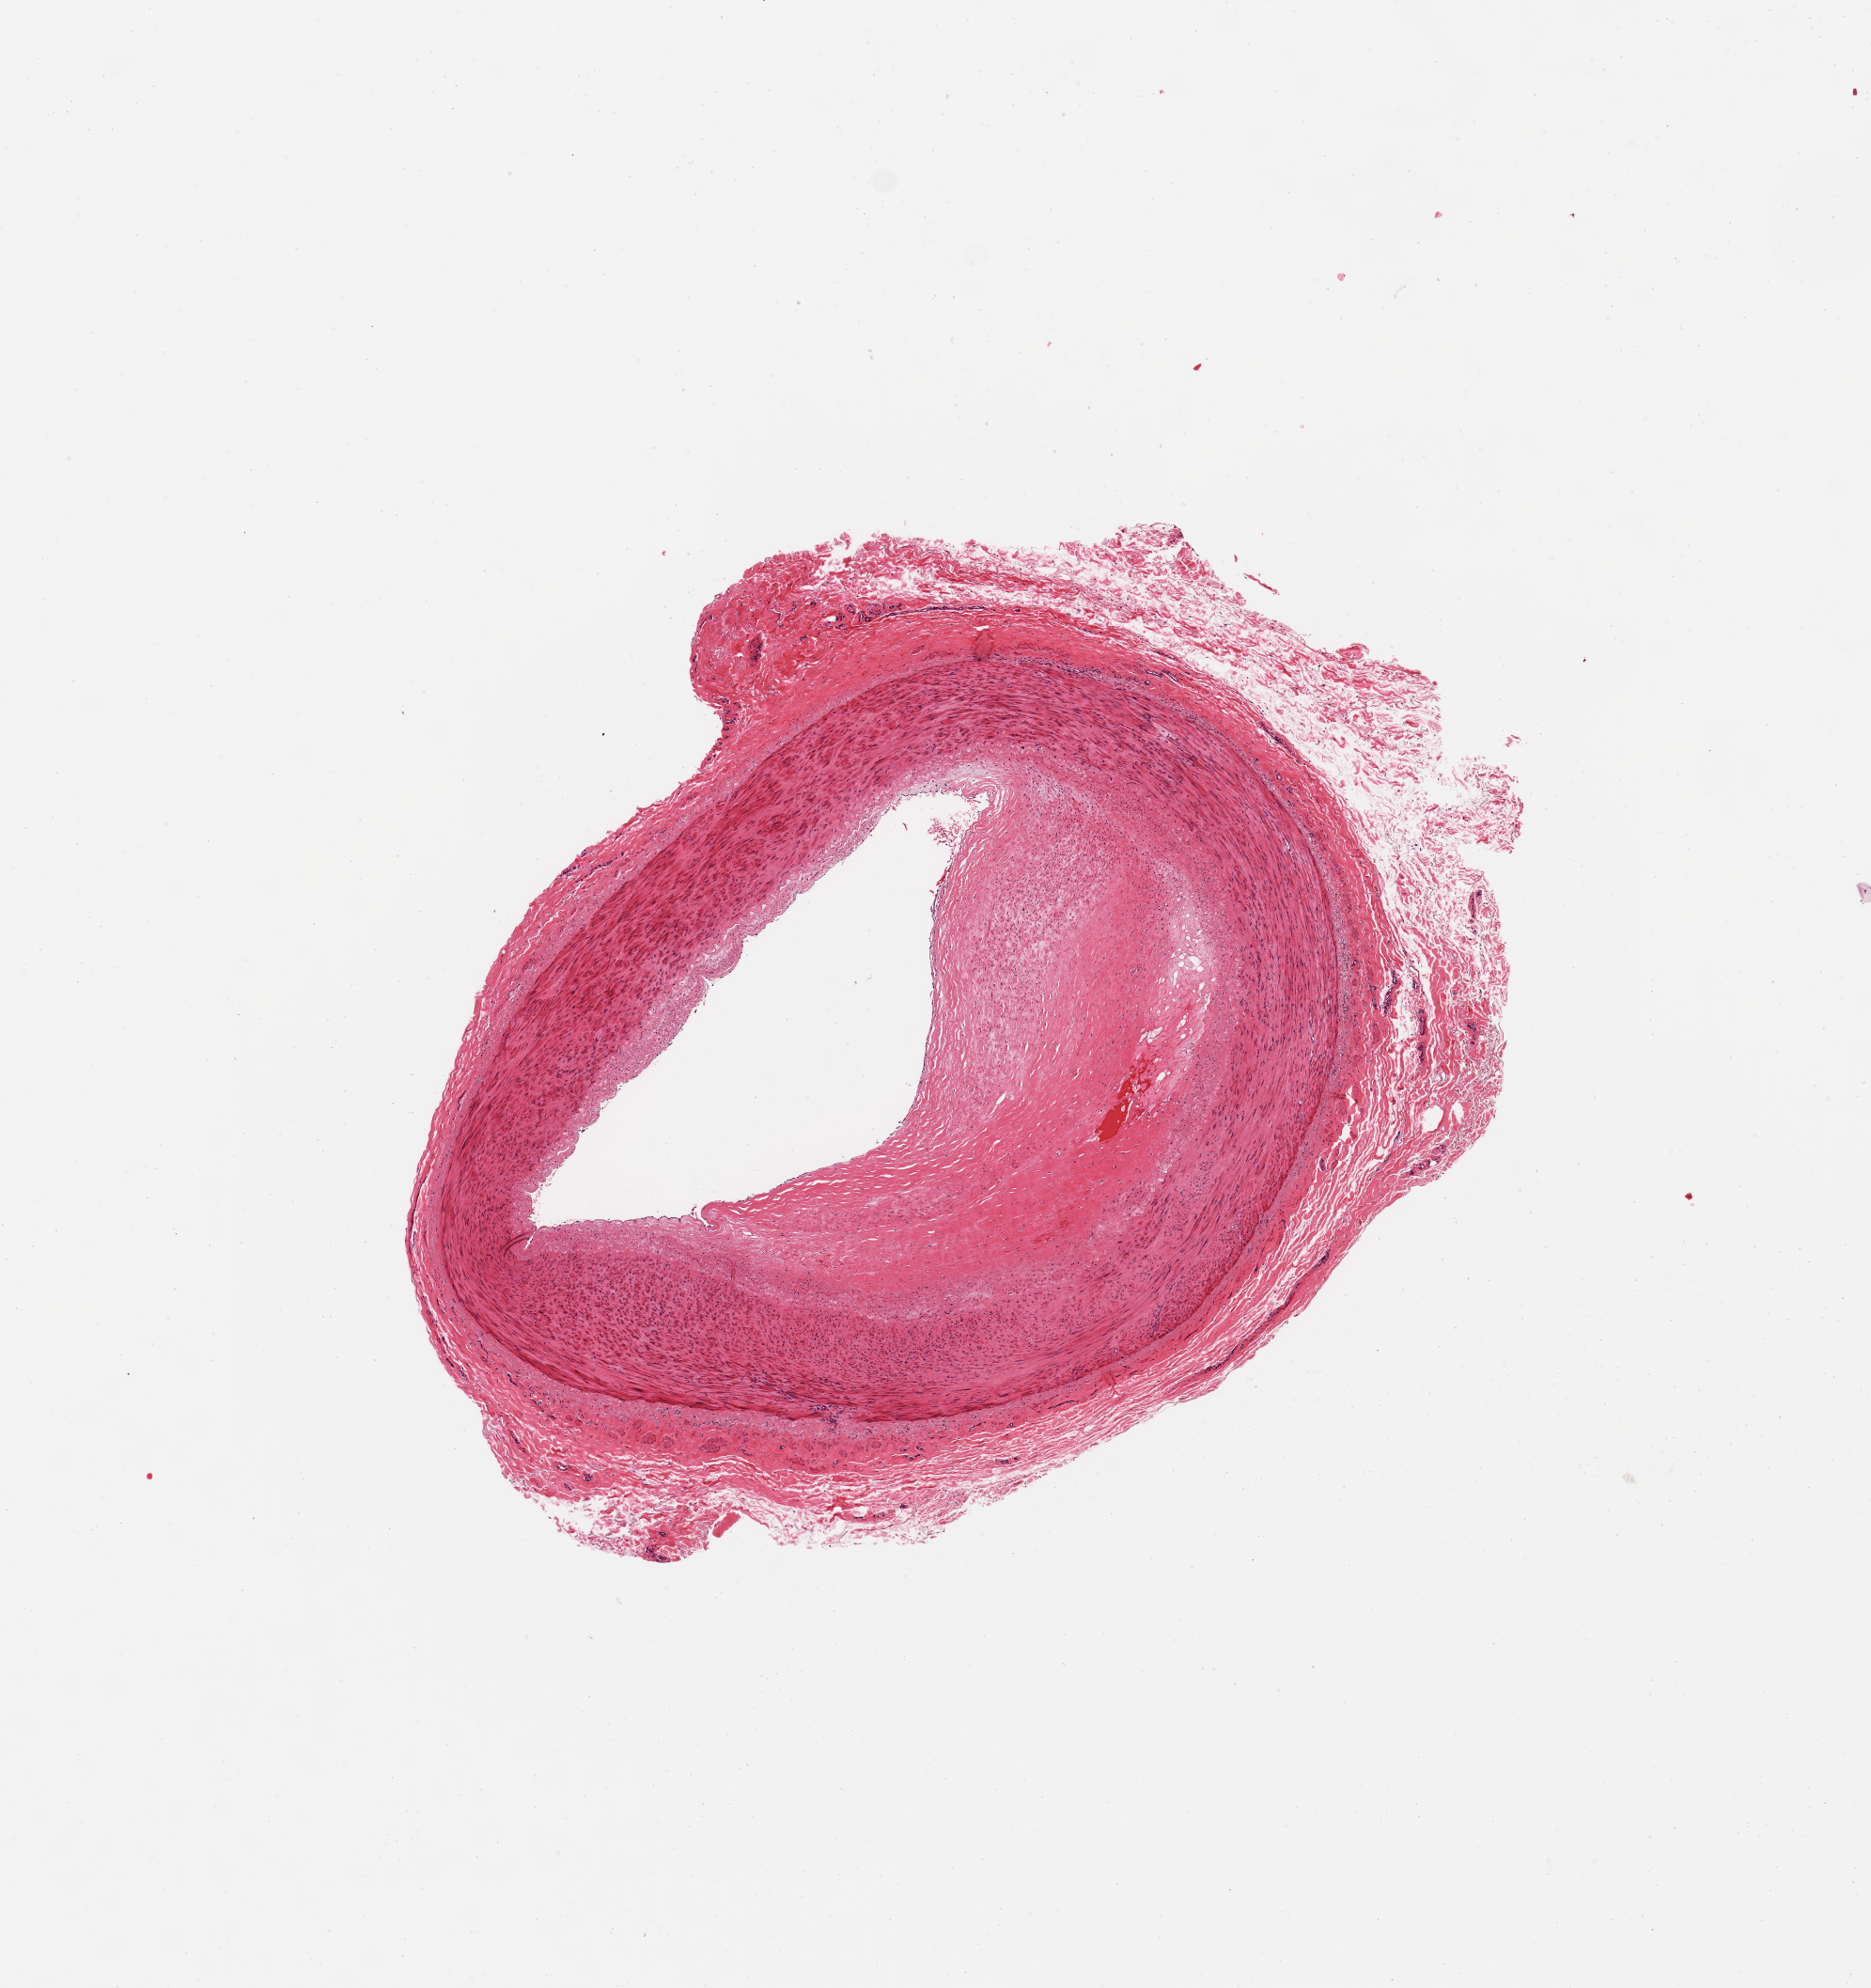
Haematoxylin and eosin whole-slide image, shown as a low-resolution overview of the whole scanned area (about 7.9 x 8.4 mm). PAXgene-fixed, paraffin-embedded tissue. Target tissue: tibial artery. Tissue donor sample.
Review note (as recorded): 1 pieces, muscular artery as with 2225; partially occlusive atherosis, ~50%.